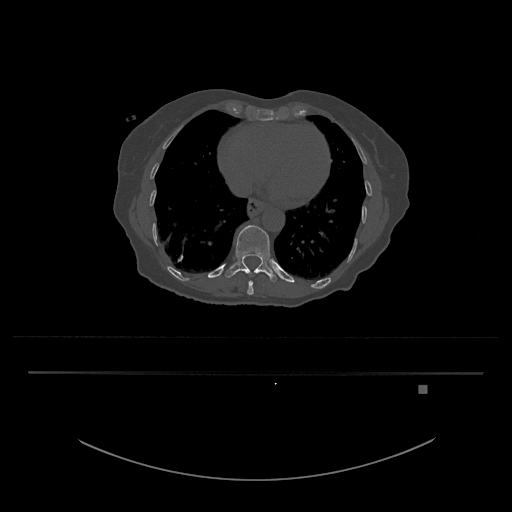
CT including the spine, one axial slice; slice 679 of 797 in the series (ordered by position); 120 kVp; bone window (W 1800 / L 400 HU); 0.5 mm slice thickness; 512 × 512 image matrix, field of view 500 × 500 mm. Female patient, age 57 years. From the clinical record (not read from this slice): primary cancer: cervical.
Structures marked on this image (semi-automatically segmented with operator editing):
- T10 vertebra: box from (x=247, y=272) to (x=254, y=295) px
- T11 vertebra: (x=224, y=225)–(x=277, y=282)